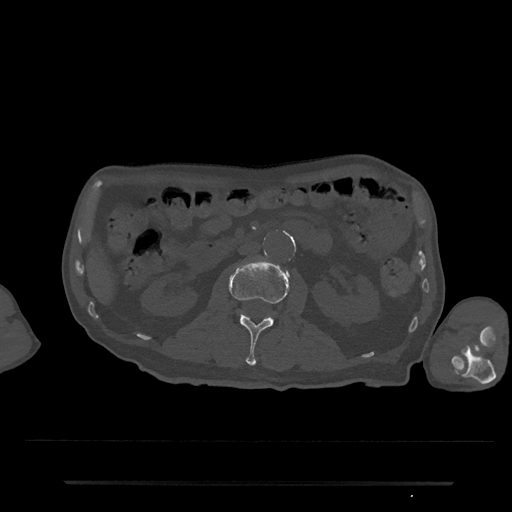
CT including the spine, one axial slice; position 44 of 797 along the scan axis; reconstruction kernel Br40s/3; bone window (W 1800 / L 400 HU); 512 × 512 image matrix. Male patient, age 74 years. From the clinical record (not read from this slice): primary cancer: prostate.
Outlined on this slice (semi-automatically segmented with operator editing):
- L2 vertebra: box from (x=228, y=258) to (x=289, y=366) px